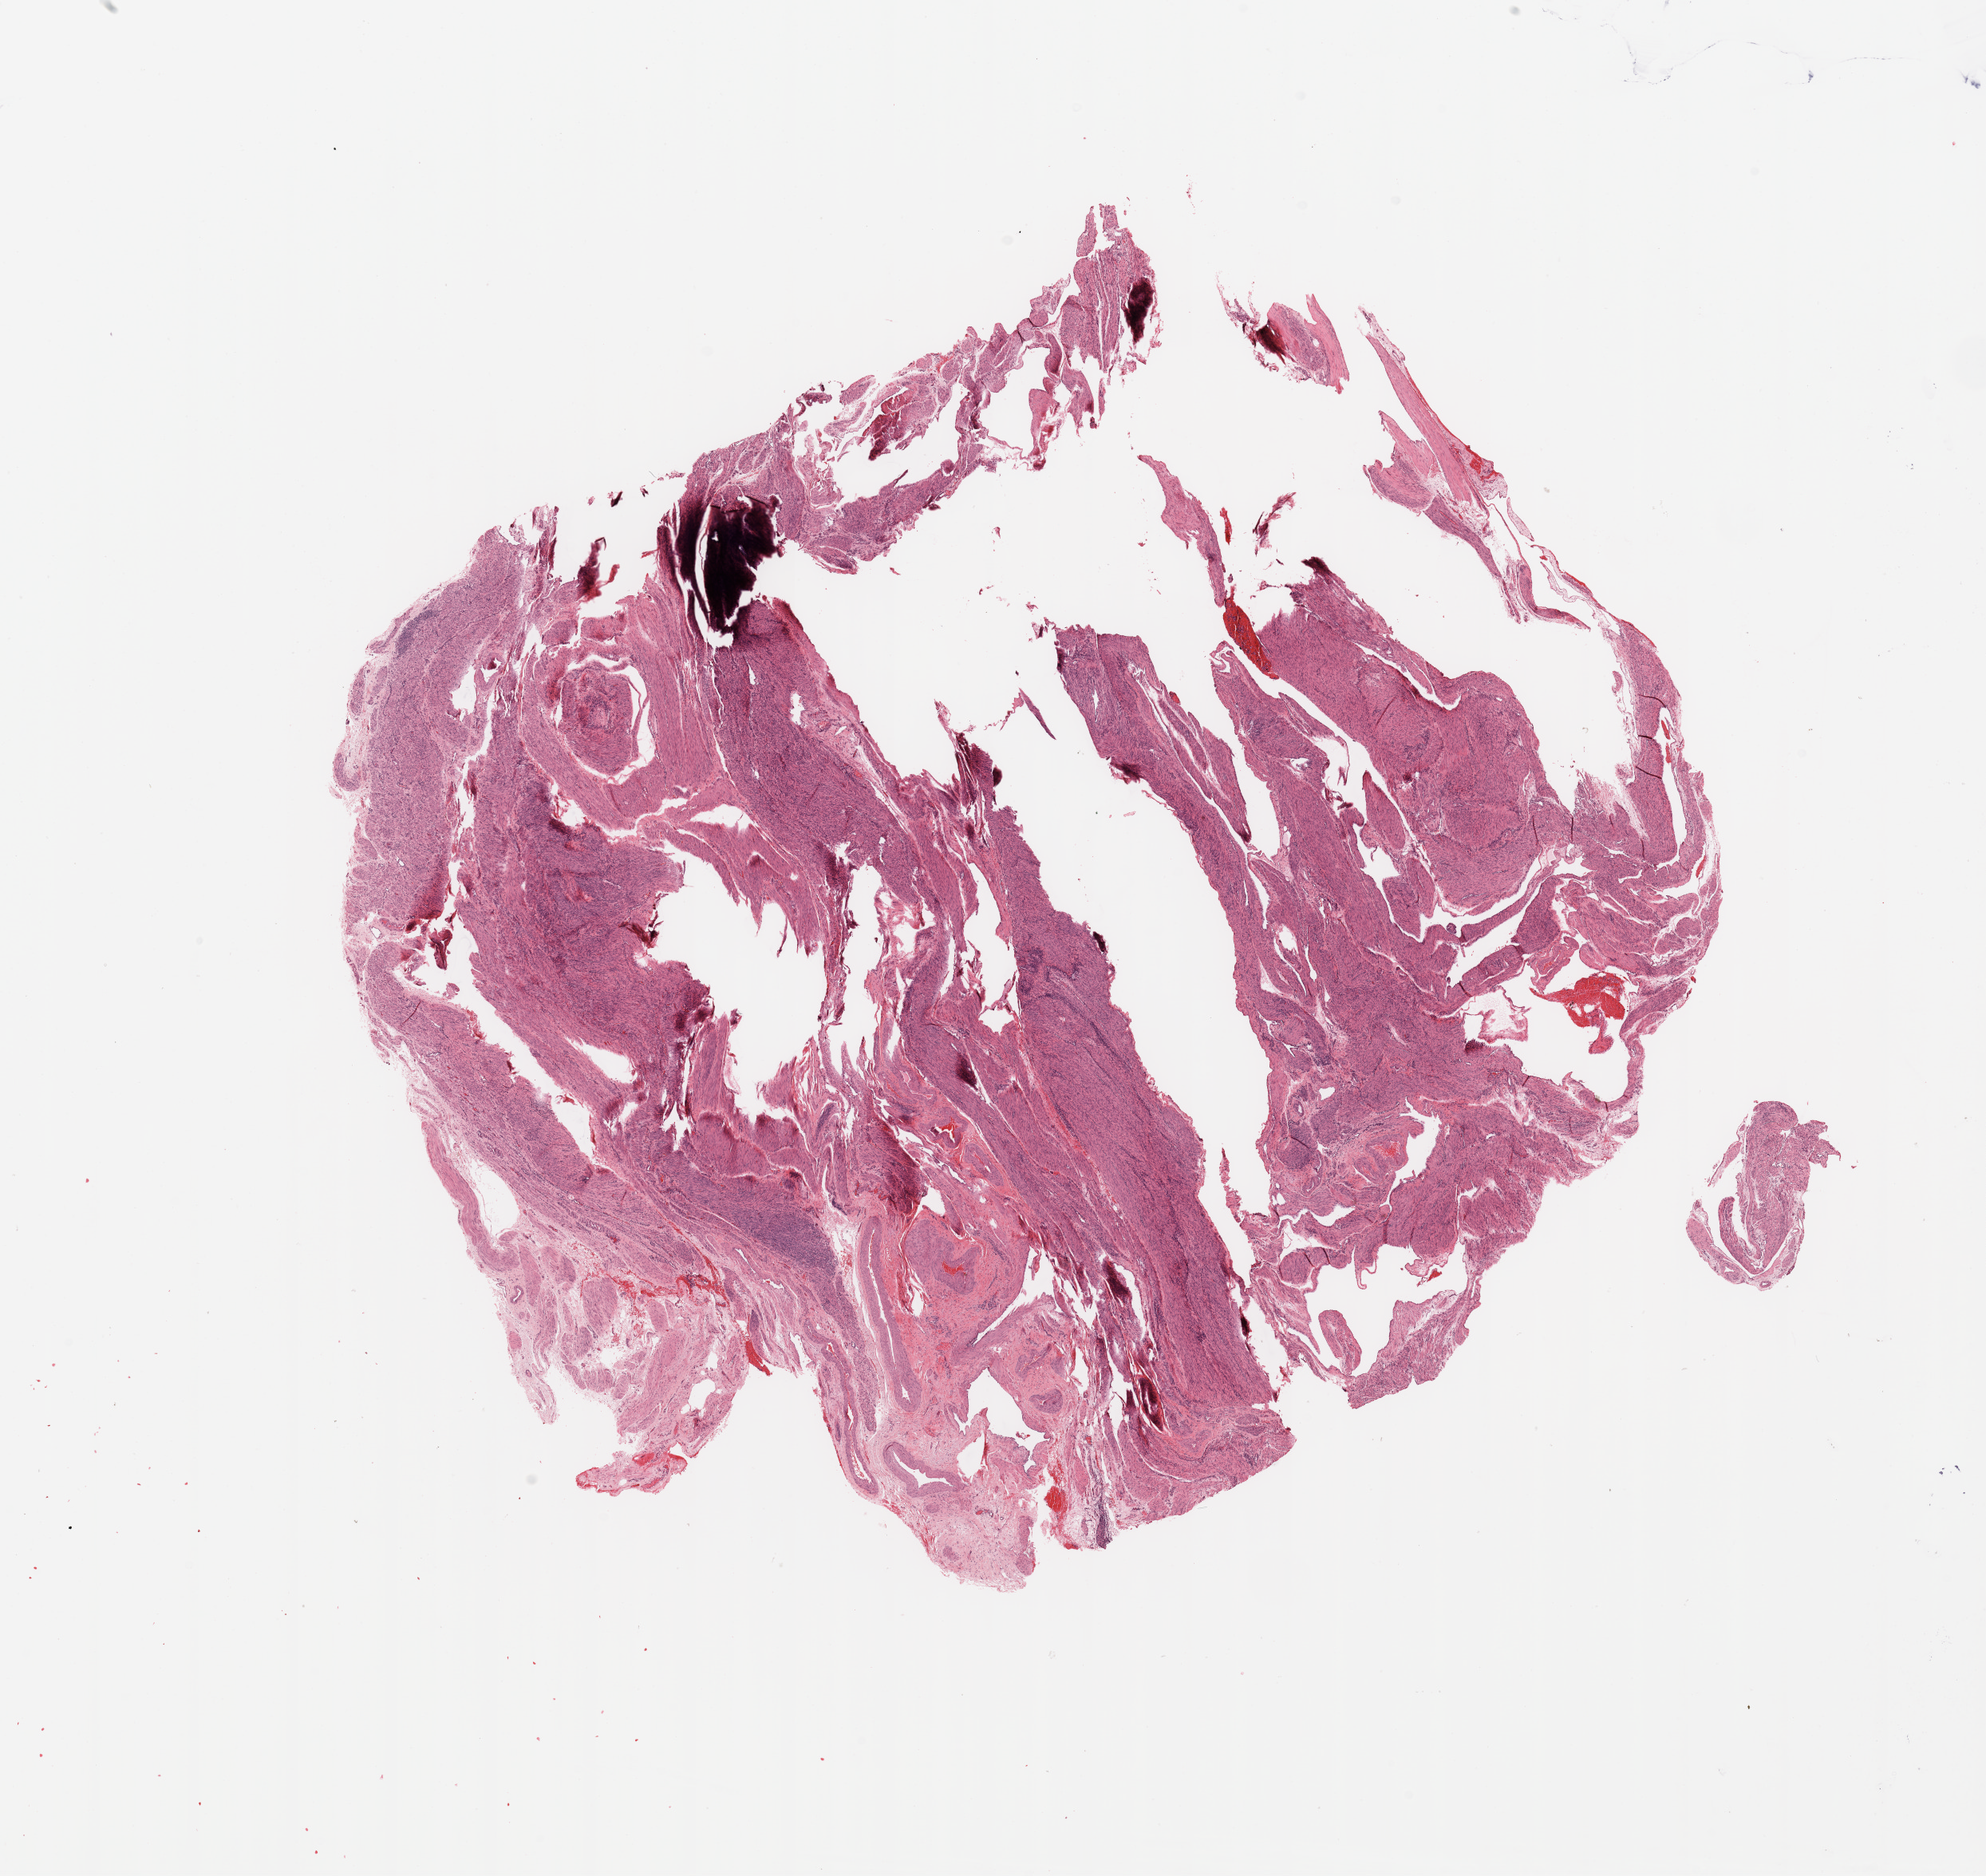
Digitized H&E-stained tissue section (whole slide) — a low-resolution overview of the entire scanned area, about 19.7 x 18.6 mm (slide scanned at 20x); uterus, normal (non-tumour) tissue. 58-year-old female patient.
This section: normal (non-tumour) tissue from the same patient. Patient diagnosis: Endometrioid adenocarcinoma, NOS.